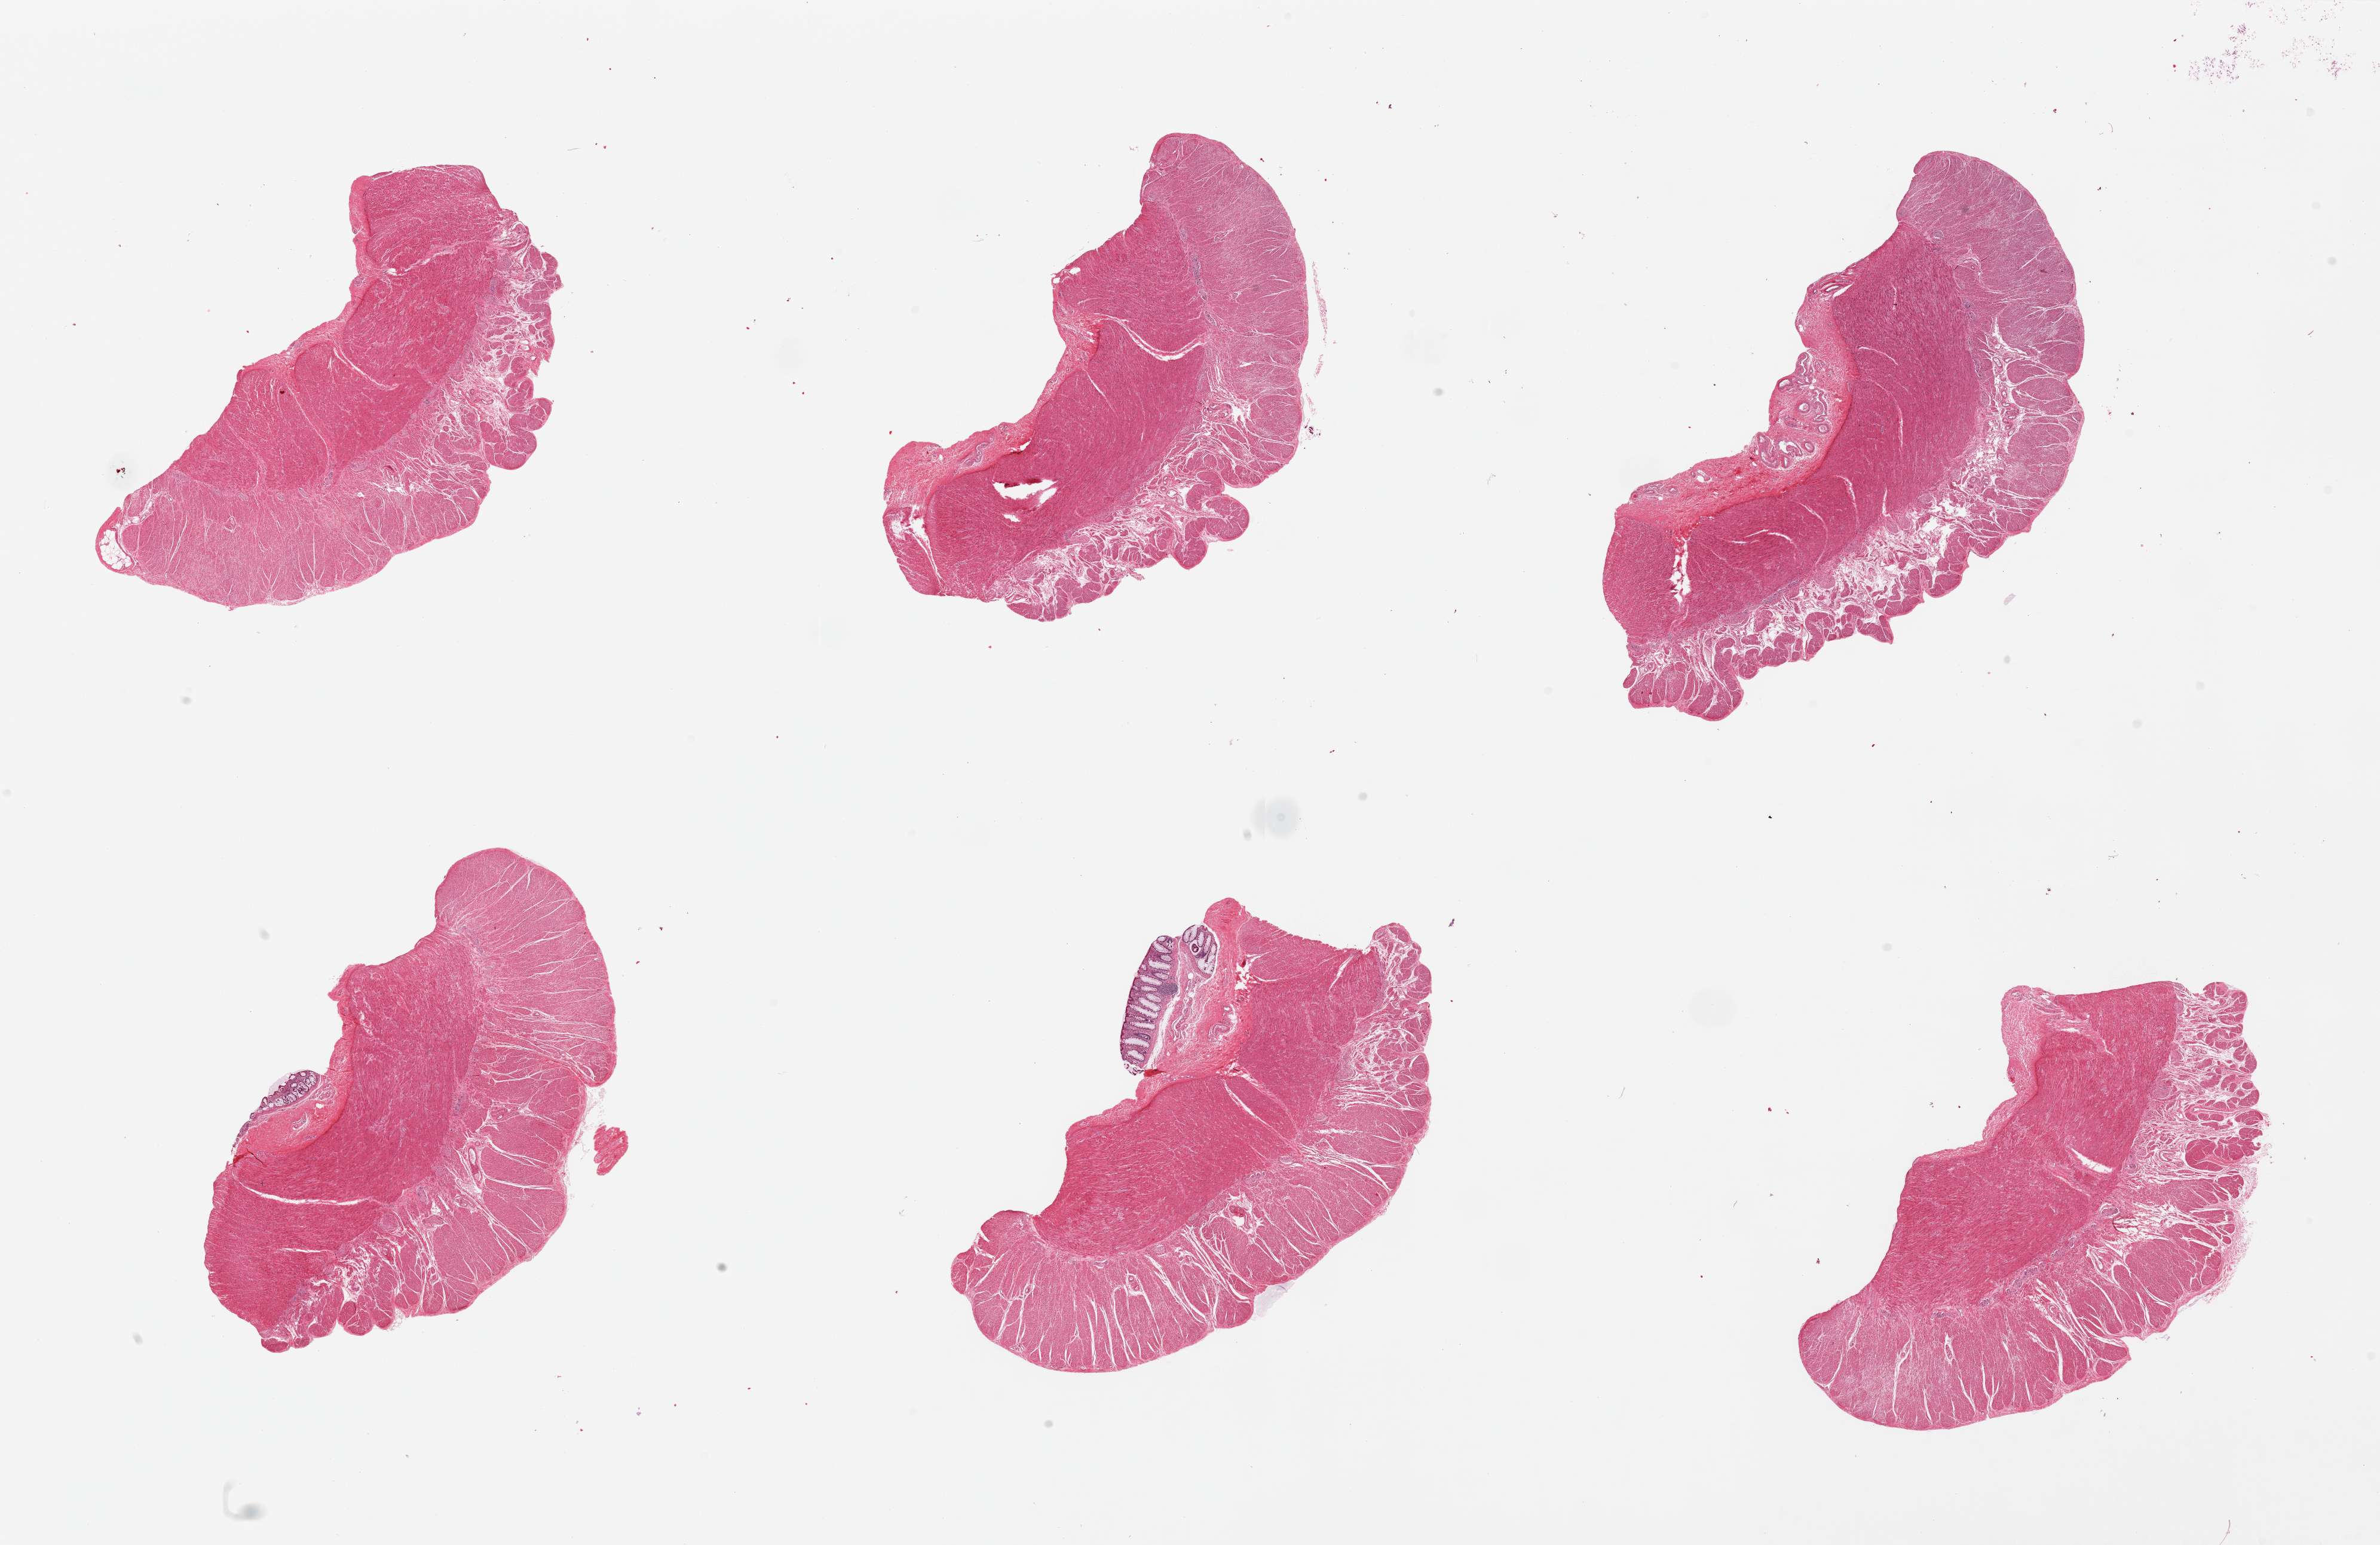
Whole-slide image, haematoxylin and eosin stain — shown as a low-resolution overview of the whole scanned area (about 31.5 x 20.4 mm, from a 20x scan), PAXgene-fixed, paraffin-embedded tissue, section of sigmoid colon (target tissue), tissue donor sample. Male donor.
Pathologist's review note for this sample: 6 pieces, two with small attachment of mucosa (not target).